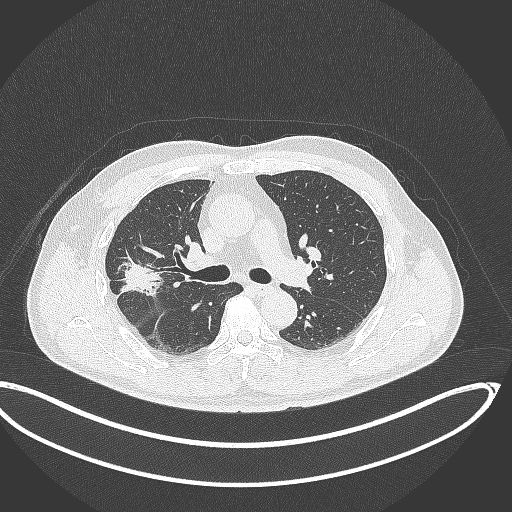
Chest CT, one axial slice; slice 211 of 391 in the series (ordered by position); 120 kVp; lung window (W 1500 / L -600 HU); 1 mm slice thickness; 512 × 512 image matrix, field of view 439 × 439 mm. Male patient, age 63 years. From the clinical record (not read from this slice): clinical TNM (as recorded): T1c N0 M0; histopathological grade: G2-3.
Annotated regions visible in this slice (rectangle marked by the reading radiologist):
- lung tumour (recorded histology: adenocarcinoma): bounding box [x1, y1, x2, y2] px = [118, 250, 167, 303]